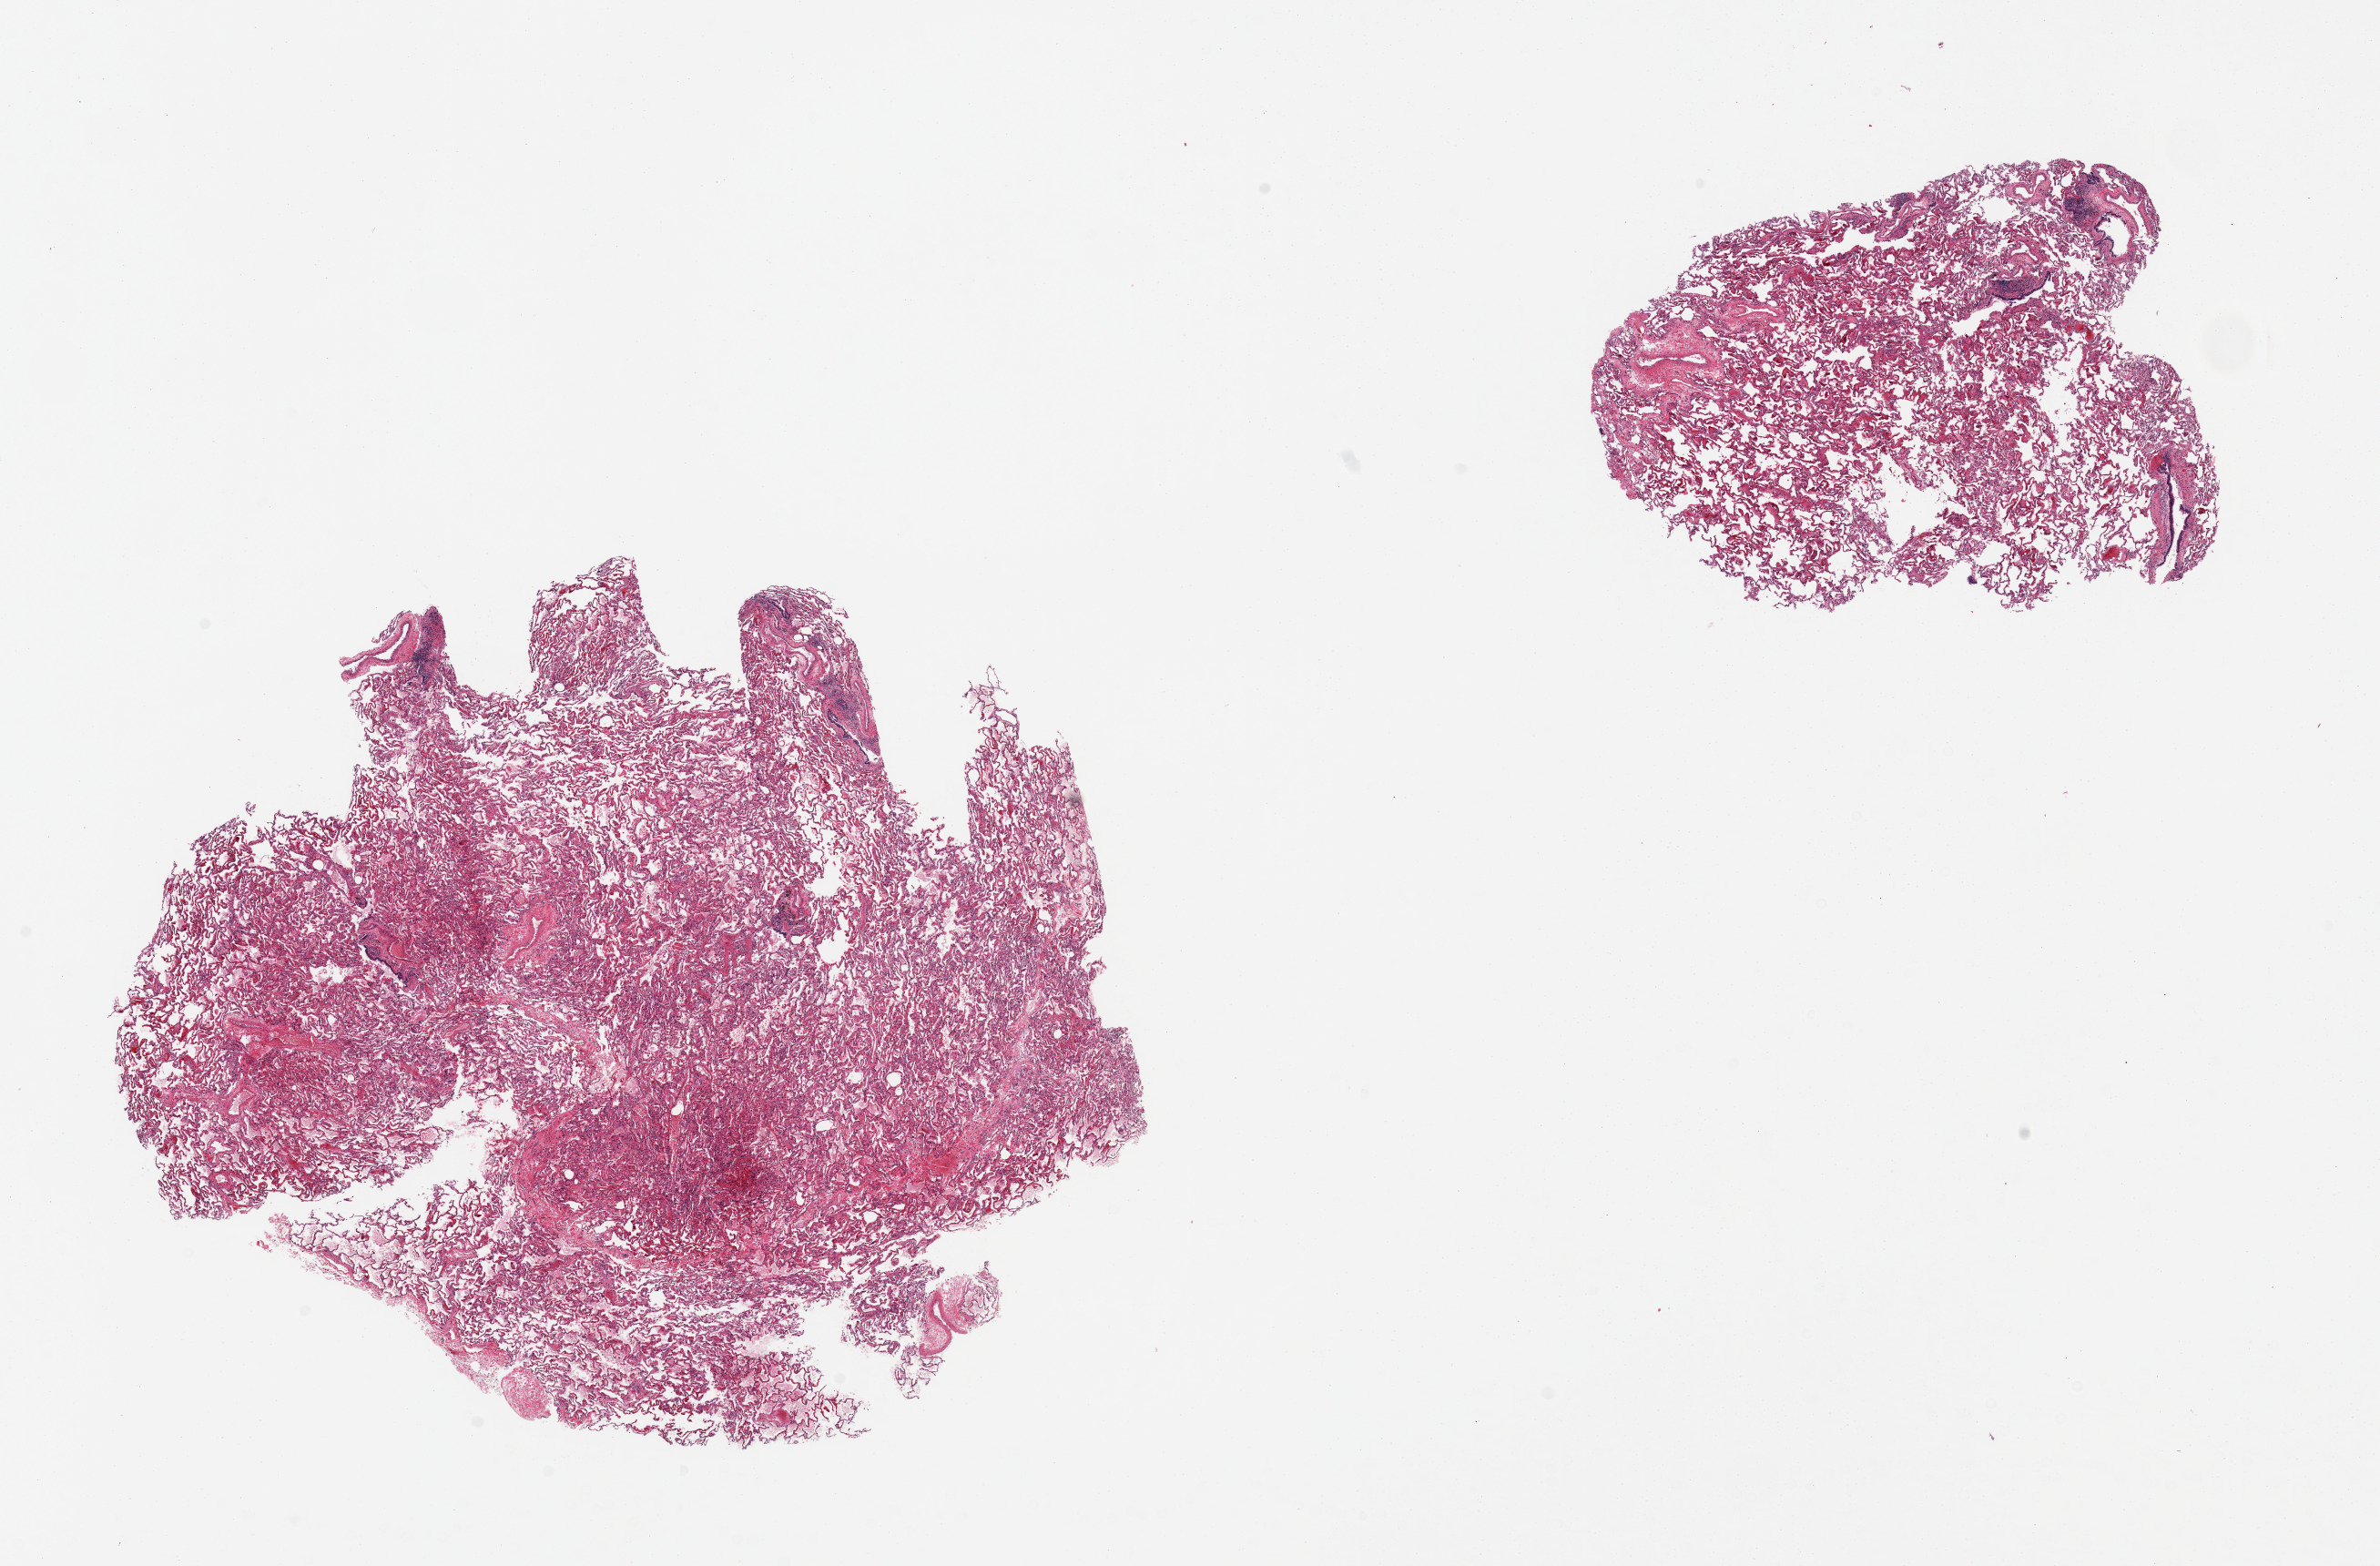
Hematoxylin and eosin (H&E) whole-slide image, a low-resolution overview of the entire scanned area, about 20.7 x 13.6 mm; PAXgene-fixed paraffin-embedded (PFPE) section; sampled site (target tissue): lung; tissue donor sample. Donor: male.
Pathologist's review note for this sample: 2 pieces; no lesions; focal alveolar fluid.